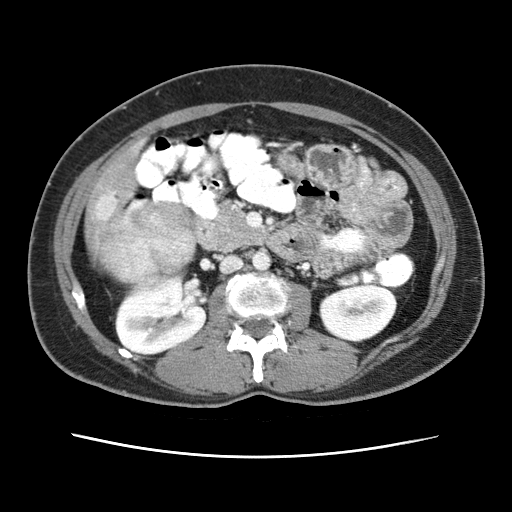
Contrast-enhanced abdominal CT (liver protocol), one axial slice. Reconstruction kernel STANDARD. Soft-tissue window (W 400 / L 40 HU). 2.5 mm slice thickness. 512 × 512 image matrix, field of view 340 × 340 mm. Case-level facts recorded for this patient, not image findings: diagnosis: hepatocellular carcinoma (patient treated with transarterial chemoembolisation; whether this scan precedes or follows treatment is not stated here); TNM stage (as recorded): Stage-I; Child-Pugh class: A; tumour nodularity: uninodular.
Annotated regions visible in this slice (semi-automatically segmented with operator editing):
- abdominal aorta: bounding box [x1, y1, x2, y2] px = [254, 252, 272, 272]
- liver parenchyma outside the tumour (the mass and vessels are separate outlines, so this box may not span the whole liver): [98, 156, 134, 201]
- mass: [96, 201, 195, 285]